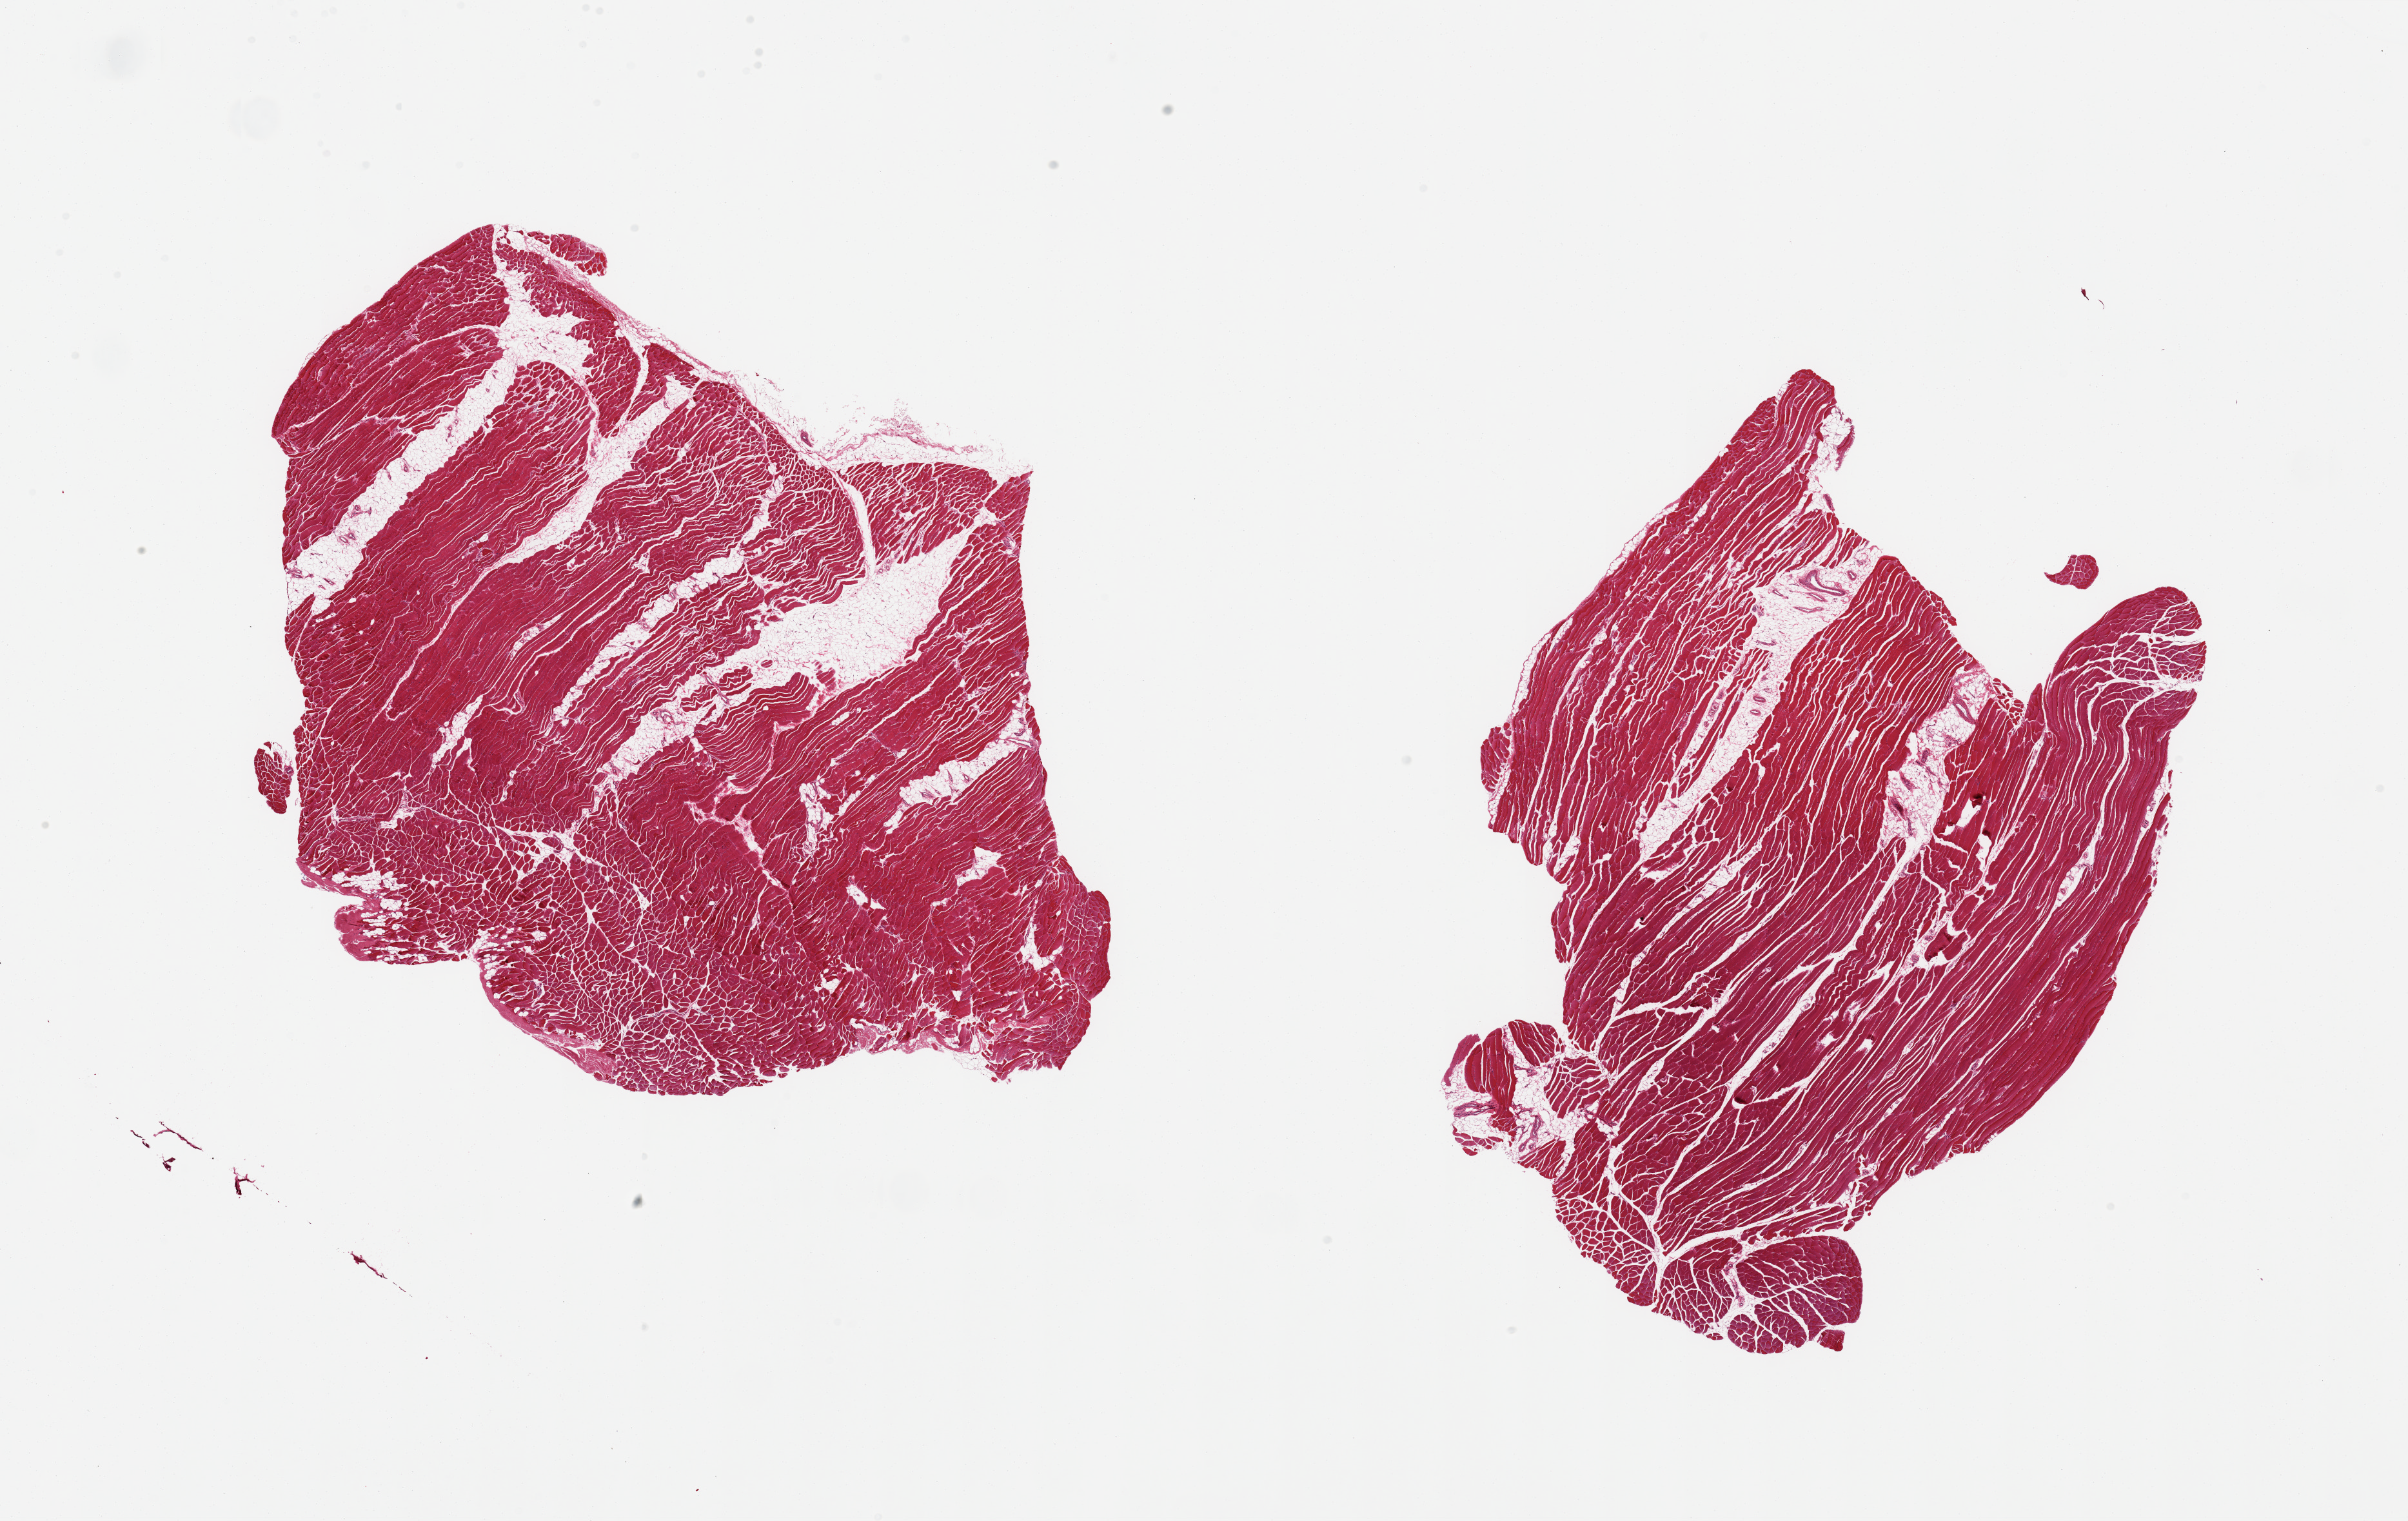
H&E whole-slide image, low-resolution overview of the scanned area, about 29.5 x 18.7 mm, PAXgene-fixed paraffin-embedded (PFPE) section, sampled site (target tissue): skeletal muscle, tissue donor sample. Donor: male.
Reviewer comment on this tissue sample: 2 pieces; from 10-20% internal fat.